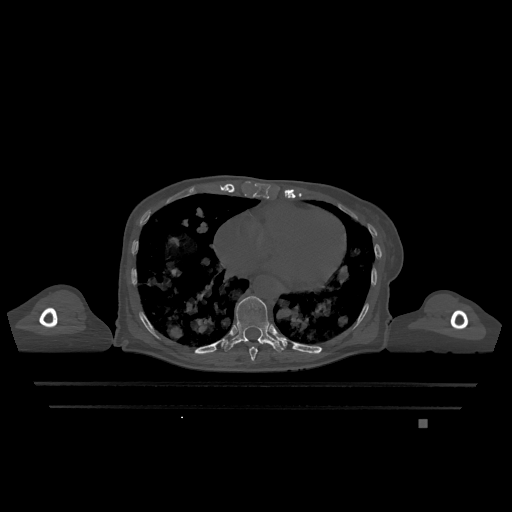
CT including the spine, one axial slice; position 659 of 1317 along the scan axis; bone window (W 1800 / L 400 HU); 0.5 mm slice thickness; 512 × 512 image matrix, field of view 500 × 500 mm. Female patient, age 74 years. Case-level facts recorded for this patient, not image findings: primary cancer: lung; vertebrae with lytic lesions (as recorded): T1, T4, T5, T6, L4, L5.
Annotated regions visible in this slice (semi-automatically segmented with operator editing):
- T10 vertebra: bounding box (x1, y1, x2, y2) in pixels: (223, 296, 283, 353)
- T9 vertebra: (249, 347, 258, 361)